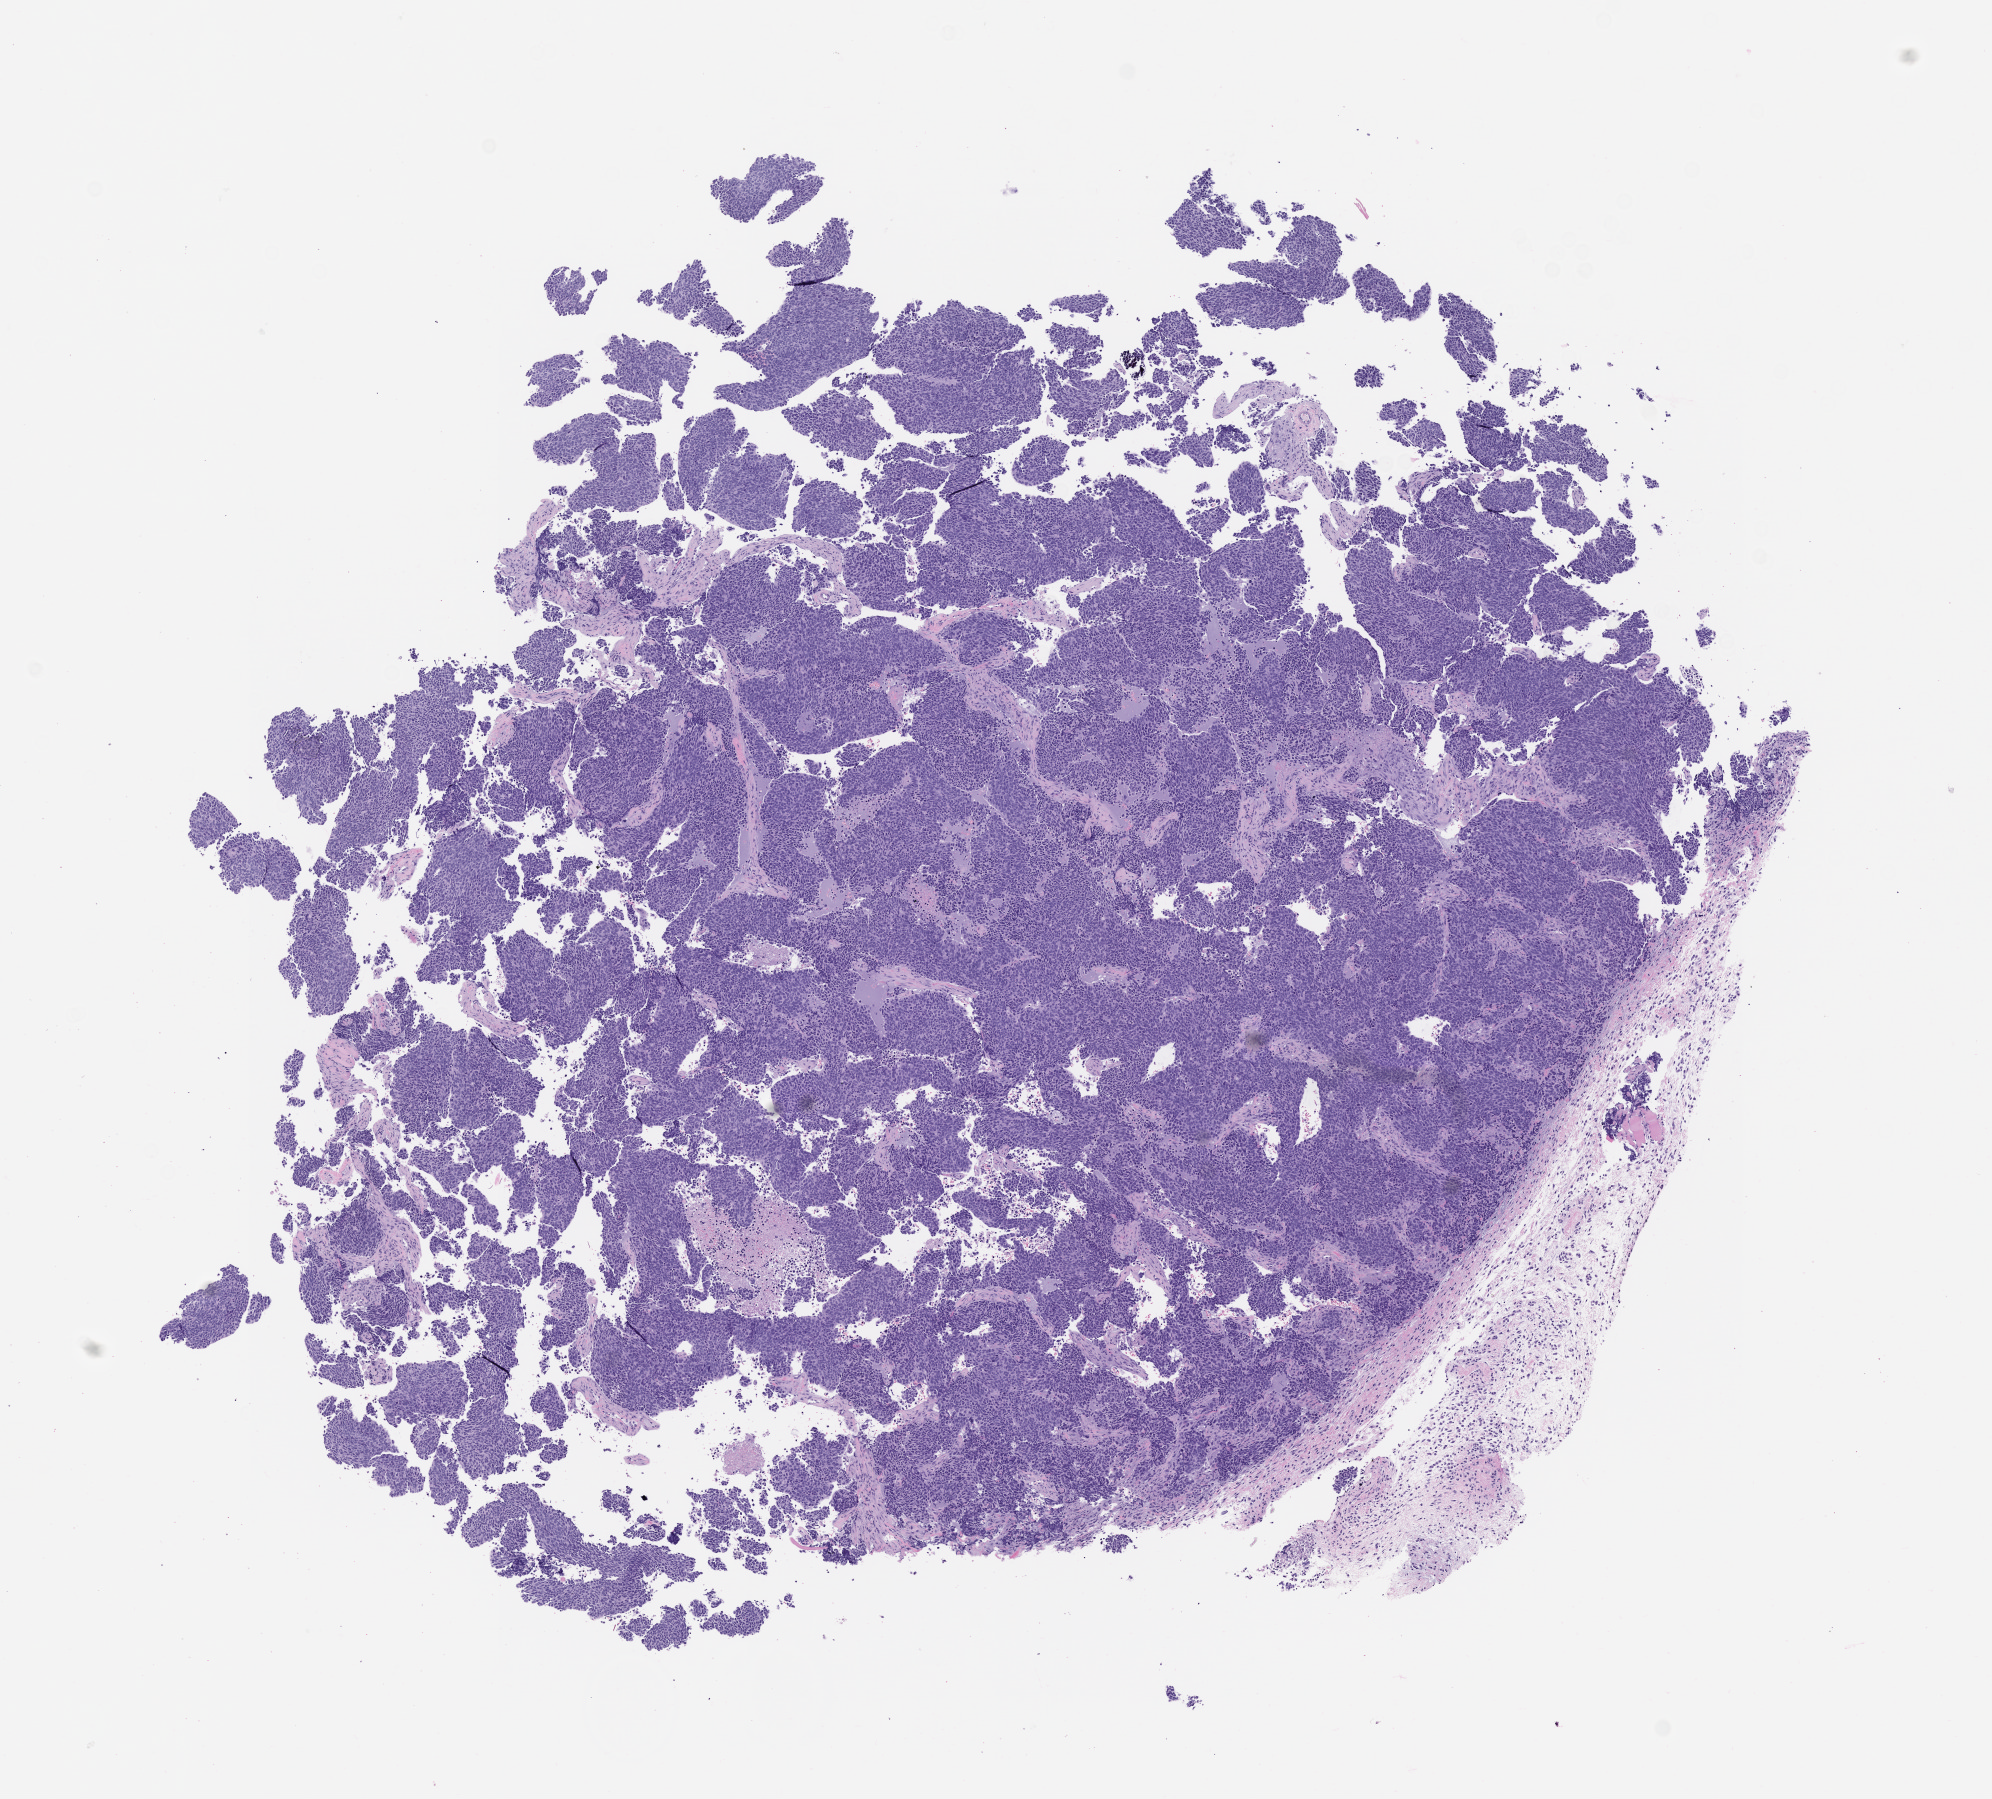
Haematoxylin and eosin whole-slide image of a patient-derived xenograft (PDX) tumor grown in a mouse, whole scanned area (about 8.0 x 7.2 mm) shown as a low-resolution overview; formalin-fixed, paraffin-embedded (FFPE) tissue; originating tumor site category: lung.
Originating patient diagnosis: Lung Adenocarcinoma.